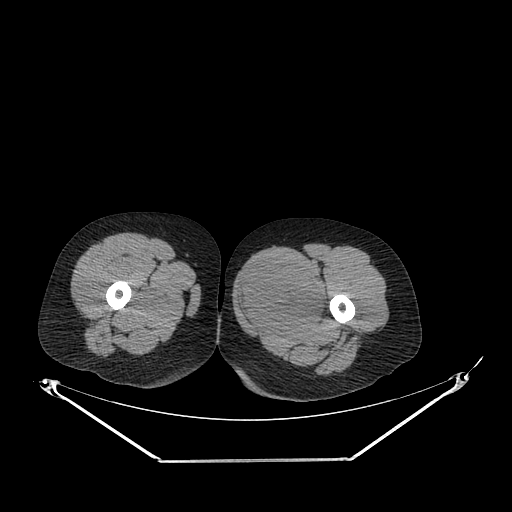
CT of an extremity soft-tissue mass (from a PET/CT study), one axial slice; position 238 of 267 along the scan axis; 120 kVp; soft-tissue window (W 400 / L 40 HU); 512 × 512 image matrix. Female patient. Case-level facts recorded for this patient, not image findings: histological type: pleiomorphic leiomyosarcoma; grade: intermediate; site of the primary tumour: left thigh.
Structures marked on this image (expert contour drawn on MRI and transferred to this co-registered scan by the dataset authors):
- gross tumour volume including surrounding oedema: bounding box (x1, y1, x2, y2) in pixels: (237, 258, 328, 332)
- gross tumour volume (mass): (237, 258, 325, 330)